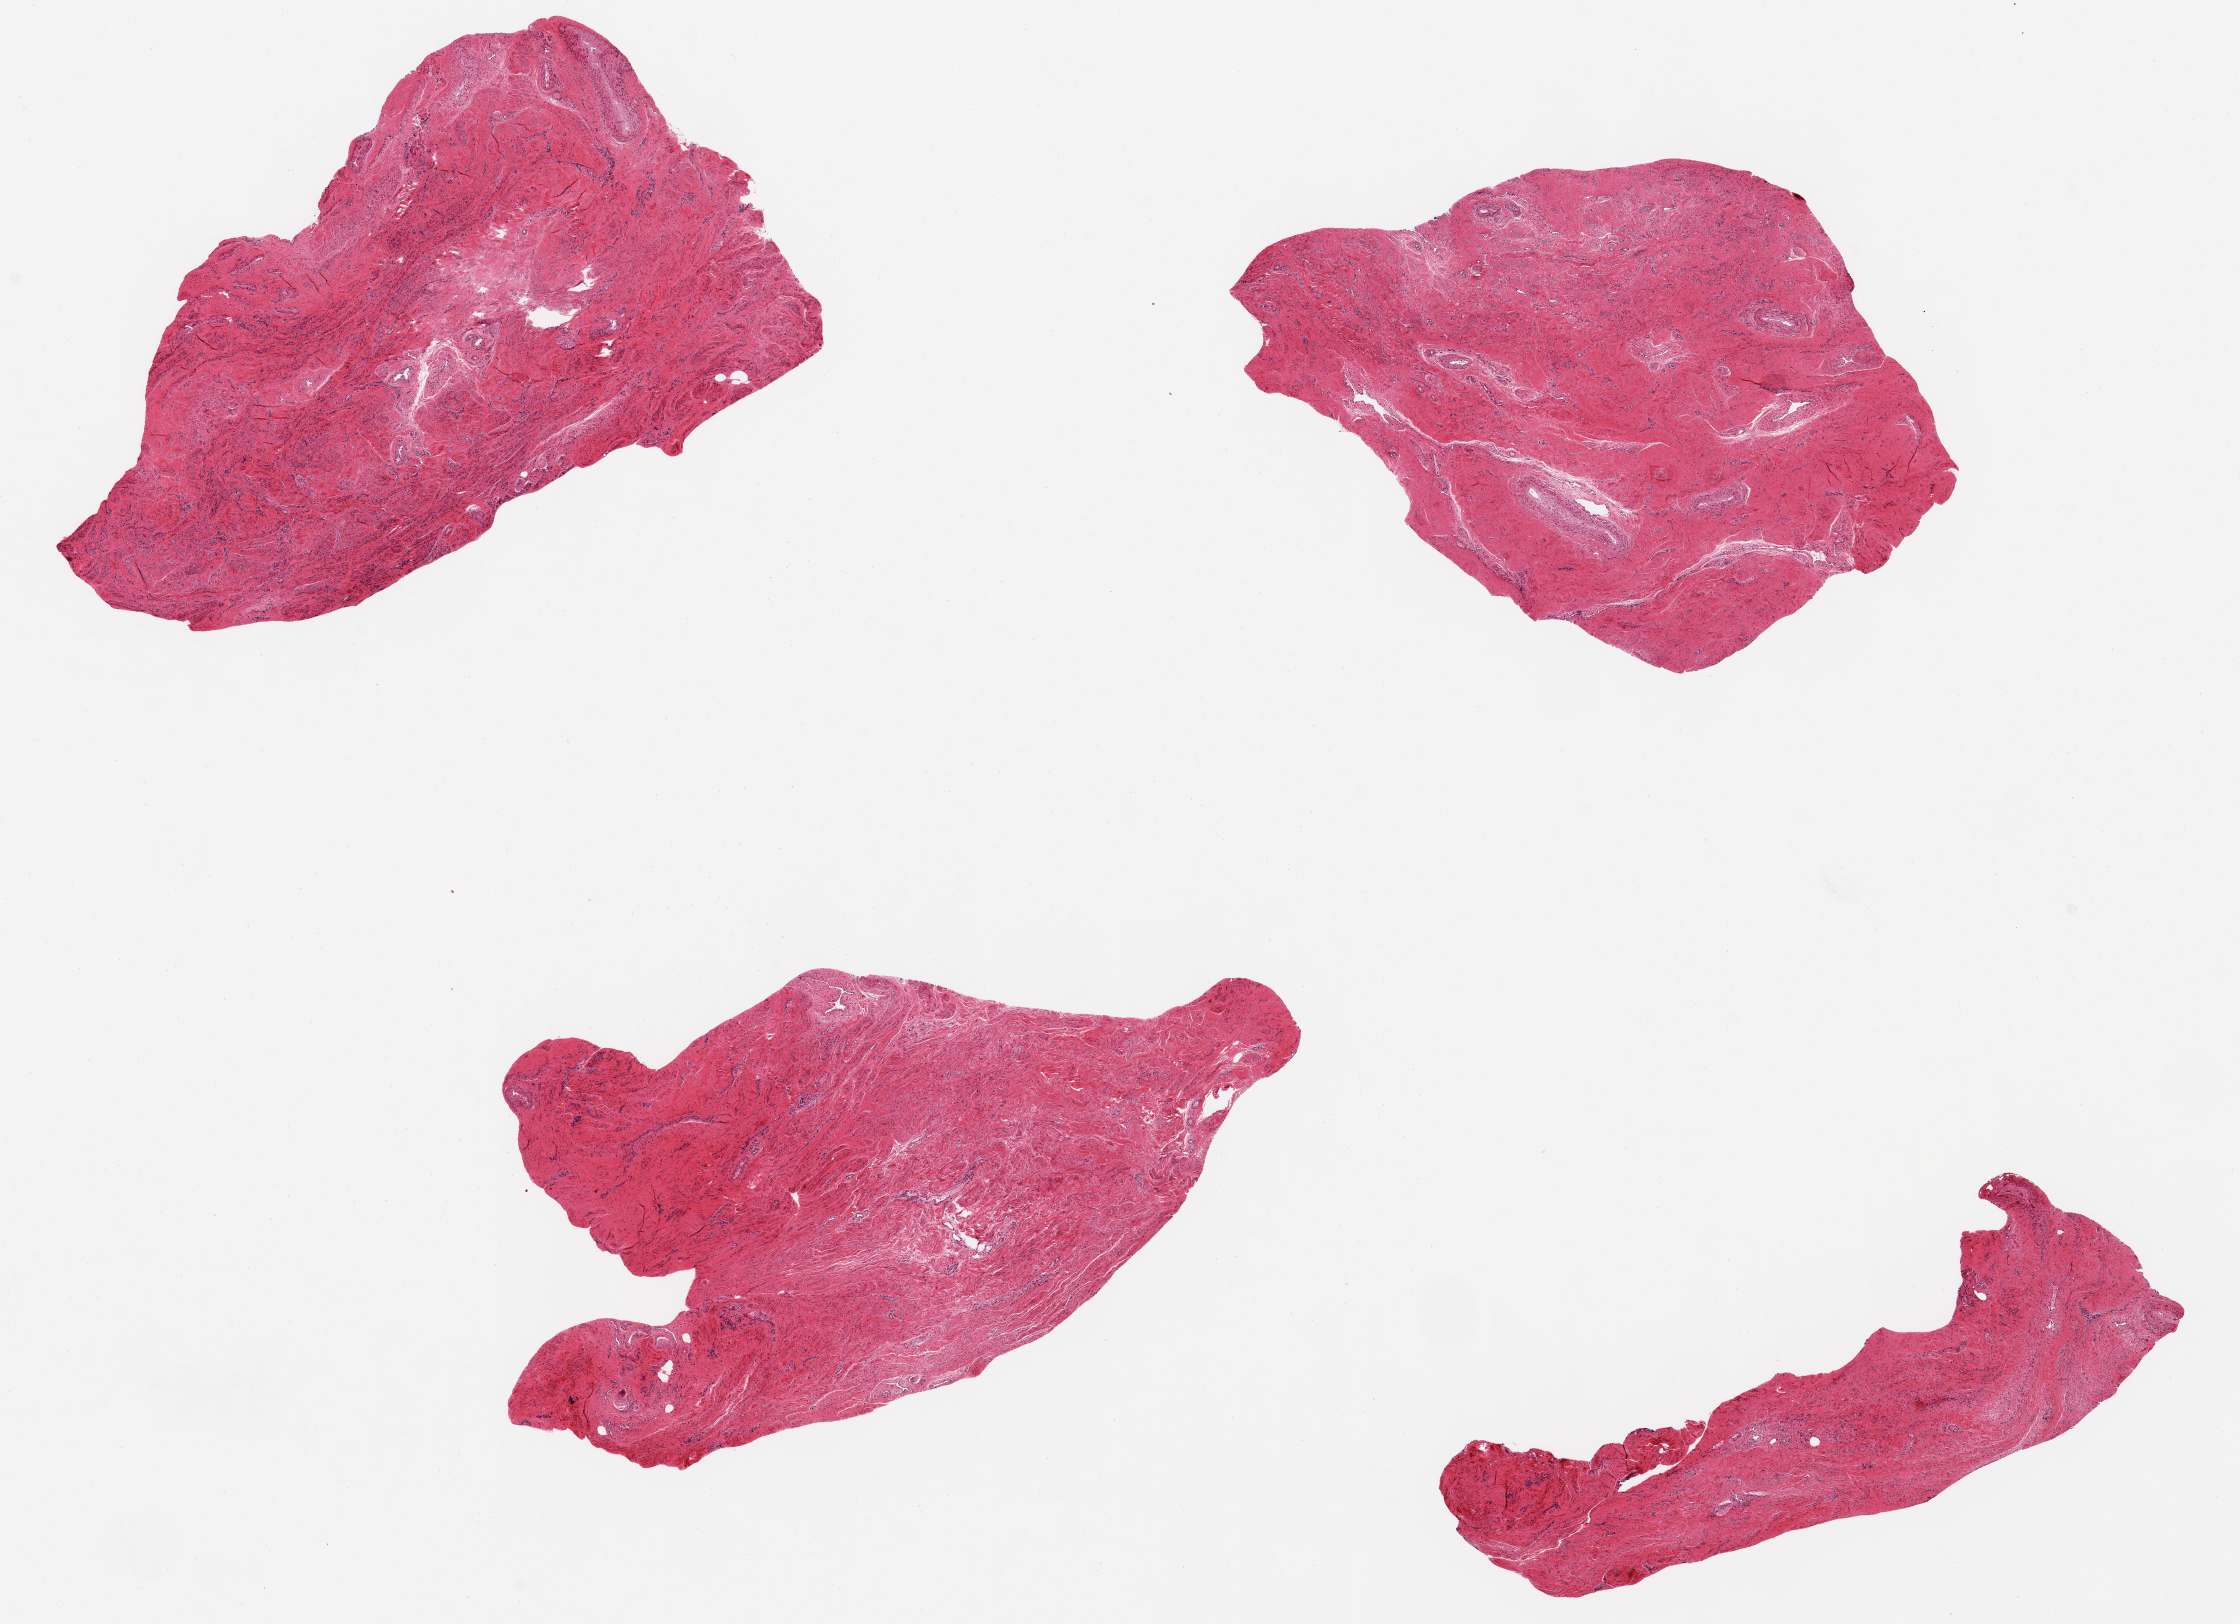
Digitized haematoxylin and eosin-stained section, whole scanned area (about 17.7 x 12.8 mm) shown as a low-resolution overview, PAXgene-fixed paraffin-embedded (PFPE) section, section of endocervix (target tissue), tissue donor sample. Female donor.
Review note (as recorded): 4 ~5x4 mm aliquots. No visible viable endo cervical mucosa.